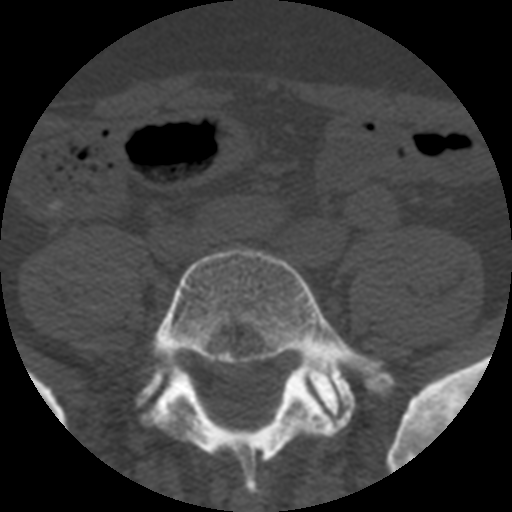
CT including the spine, one axial slice. Slice 62 of 508 in the series (ordered by position). Reconstruction kernel STANDARD. 120 kVp. Bone window (W 1800 / L 400 HU). 512 × 512 image matrix, field of view 160 × 160 mm. Patient age 57 years. Case-level facts recorded for this patient, not image findings: primary cancer: prostate.
Annotated regions visible in this slice (semi-automatic segmentation, software-assisted and operator-edited):
- L5 vertebra: box from (x=144, y=248) to (x=387, y=495) px